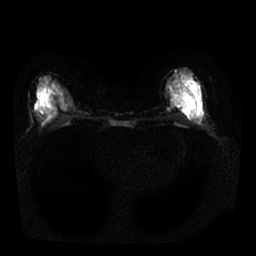
Breast MRI, one axial slice; position 11 of 25 along the scan axis; diffusion-weighted series; image 2 of 4 stored at this slice position (different b-values; order by instance number); 1.5 T; 256 × 256 image matrix, field of view 320 × 320 mm. Female patient.
Annotated regions visible in this slice (expert manual segmentation):
- tumour on diffusion-weighted imaging: box from (x=185, y=95) to (x=193, y=110) px